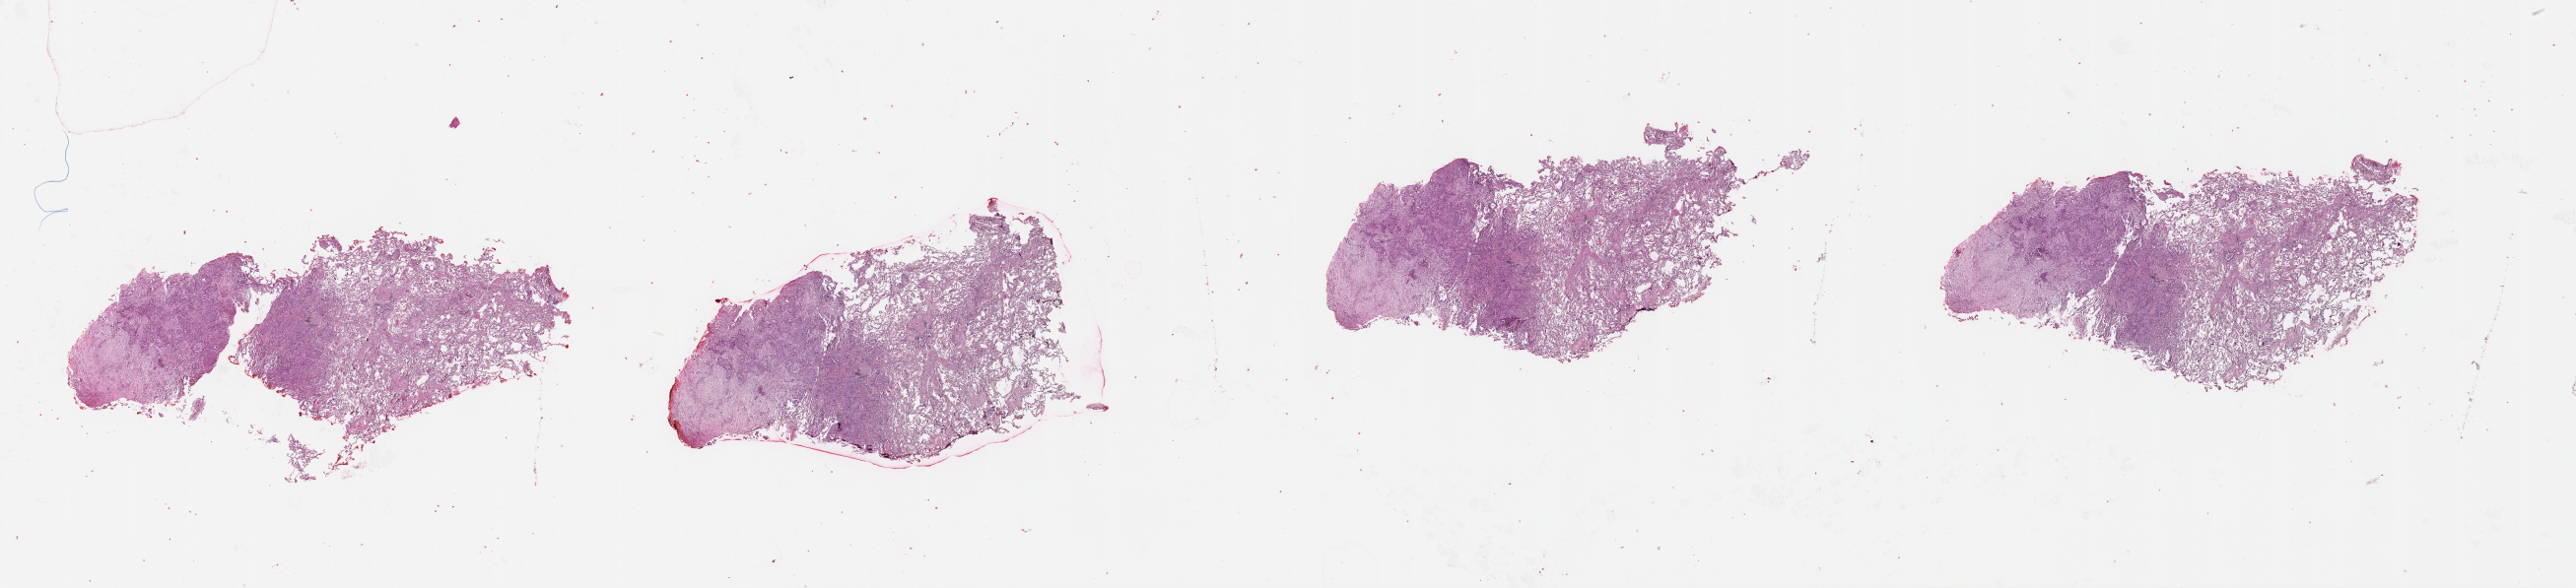
Whole-slide histology image, H&E — low-resolution overview of the scanned area, about 42.1 x 9.6 mm (acquisition: 20x scan), lung, tissue type not recorded.
• patient diagnosis (cohort enrolment): lung adenocarcinoma (lung)